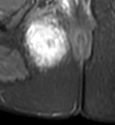
MRI of an extremity soft-tissue mass, one axial slice; slice 29 of 49 in the series (ordered by position); STIR; MR volume resampled by the dataset authors to the PET/CT grid (not the native acquisition matrix); 3.27 mm slice thickness; 115 × 125 image matrix, field of view 112 × 122 mm. Female patient. Case-level facts recorded for this patient, not image findings: histological type: epithelioid sarcoma; grade: intermediate; site of the primary tumour: right buttock.
Outlined on this slice (expert contour drawn on MRI and transferred to this co-registered scan by the dataset authors):
- gross tumour volume including surrounding oedema: bounding box [x1, y1, x2, y2] px = [24, 14, 68, 65]
- gross tumour volume (mass): [27, 23, 61, 60]